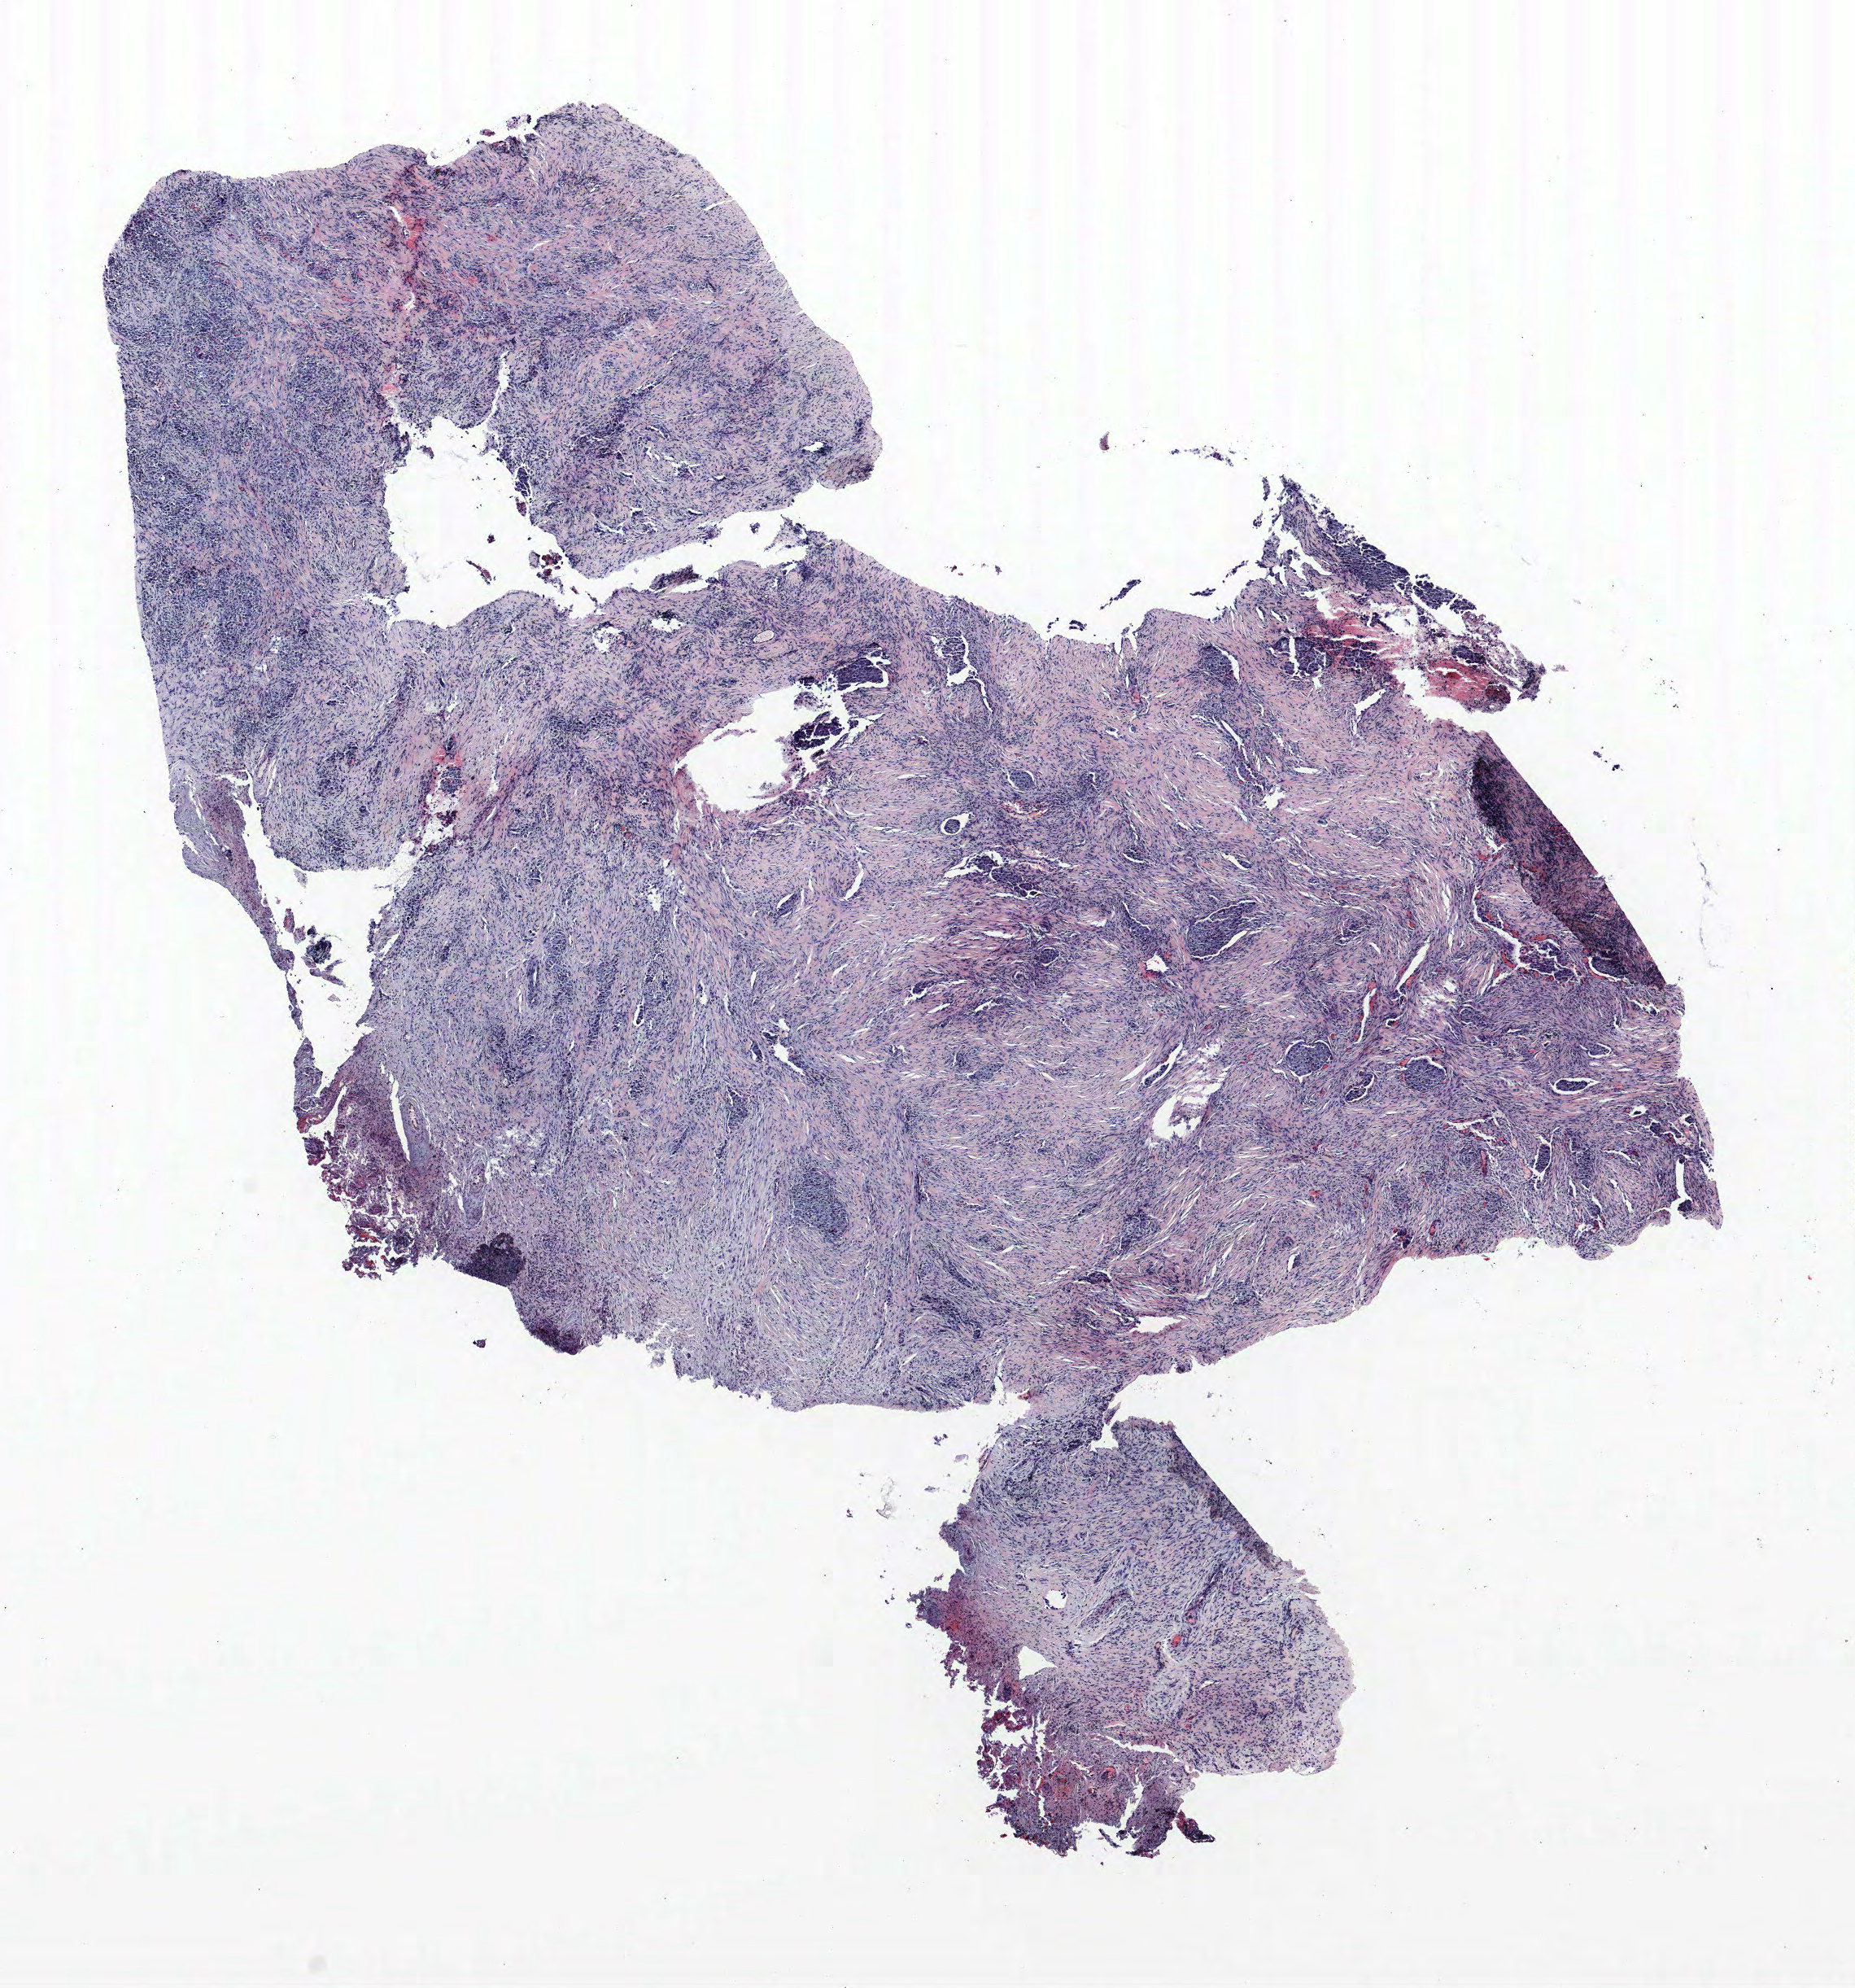
Hematoxylin and eosin (H&E) stained whole-slide image — a low-resolution overview of the entire scanned area, about 9.1 x 9.8 mm. FFPE section. Lung tissue. Female patient, aged 70 at enrolment. Former smoker at enrolment.
Stage (AJCC 6th edition): IV. Tumour size (pathology): 30 mm. Primary tumour location (clinical record): right upper lobe. Participant's lung-cancer diagnosis: Non-small cell carcinoma.